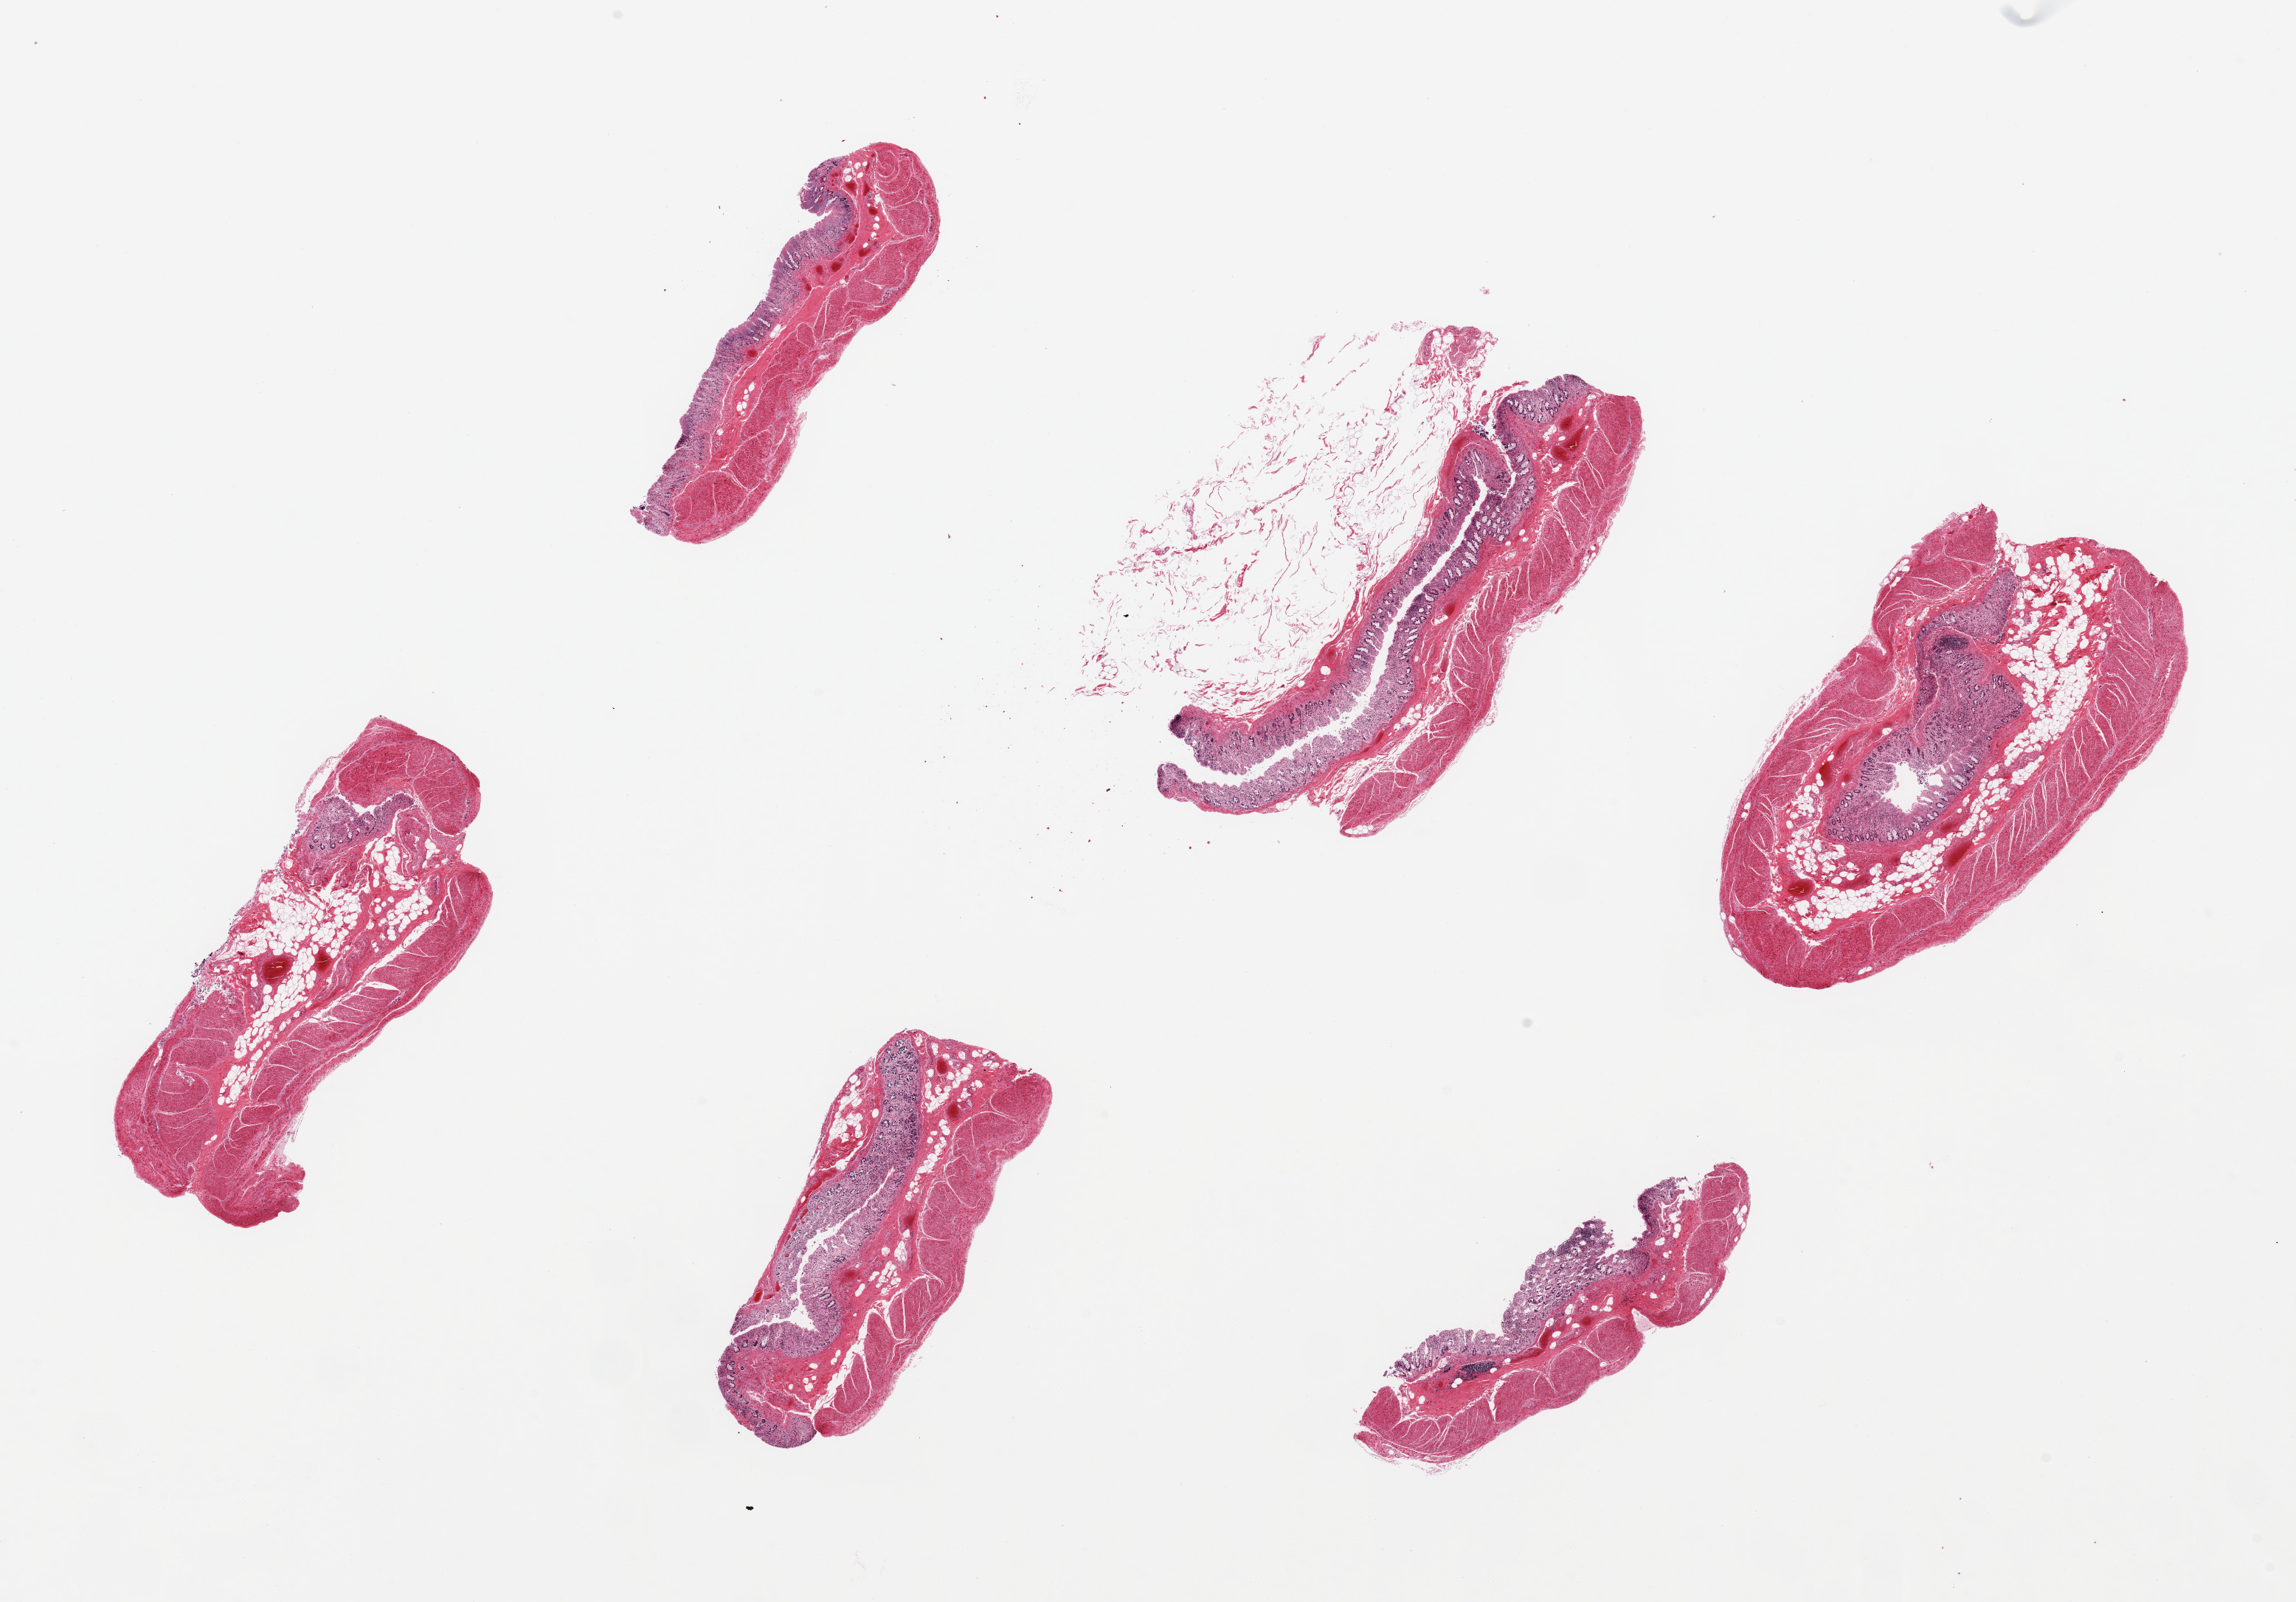
Digitized H&E-stained section — a low-resolution overview of the entire scanned area, about 24.6 x 17.2 mm, PAXgene-fixed paraffin-embedded (PFPE) section, sampled site (target tissue): transverse colon, donor tissue sample.
Reviewer comment on this tissue sample: 6 pieces ~6x2mm. Mucosa ~ 20-30% of thickness, epithelial components totally autolyzed, partially sloughed.